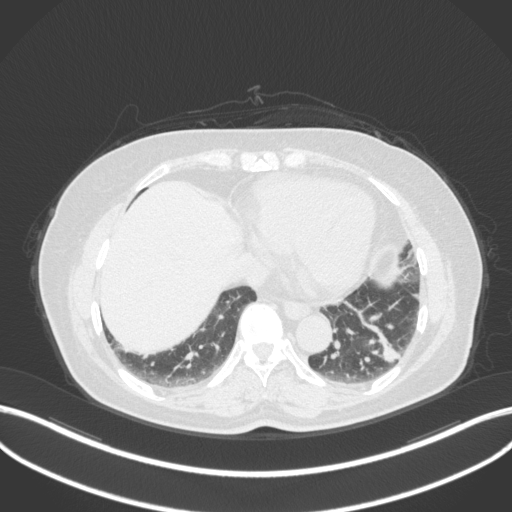
Chest CT, one axial slice. Position 116 of 307 along the scan axis. Reconstruction kernel B31f. 120 kVp. Lung window (W 1500 / L -600 HU). 1 mm slice thickness. 512 × 512 image matrix, field of view 400 × 400 mm. Patient: female, 59 years. Case-level facts recorded for this patient, not image findings: clinical TNM (as recorded): T2a N0 M0; histopathological grade: G2-3.
Outlined on this slice (rectangle marked by the reading radiologist):
- lung tumour (recorded histology: adenocarcinoma): box from (x=351, y=316) to (x=401, y=367) px